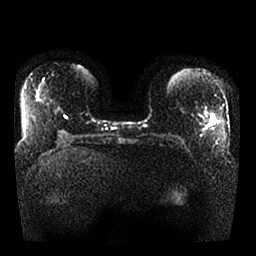
Breast MRI, one axial slice; slice 14 of 25 in the series (ordered by position); diffusion-weighted series; image 2 of 4 stored at this slice position (different b-values; order by instance number); 1.5 T; 4 mm slice thickness; 256 × 256 image matrix, field of view 340 × 340 mm. Female patient.
Structures marked on this image (manually delineated by an expert):
- tumour on diffusion-weighted imaging: box from (x=211, y=123) to (x=215, y=125) px